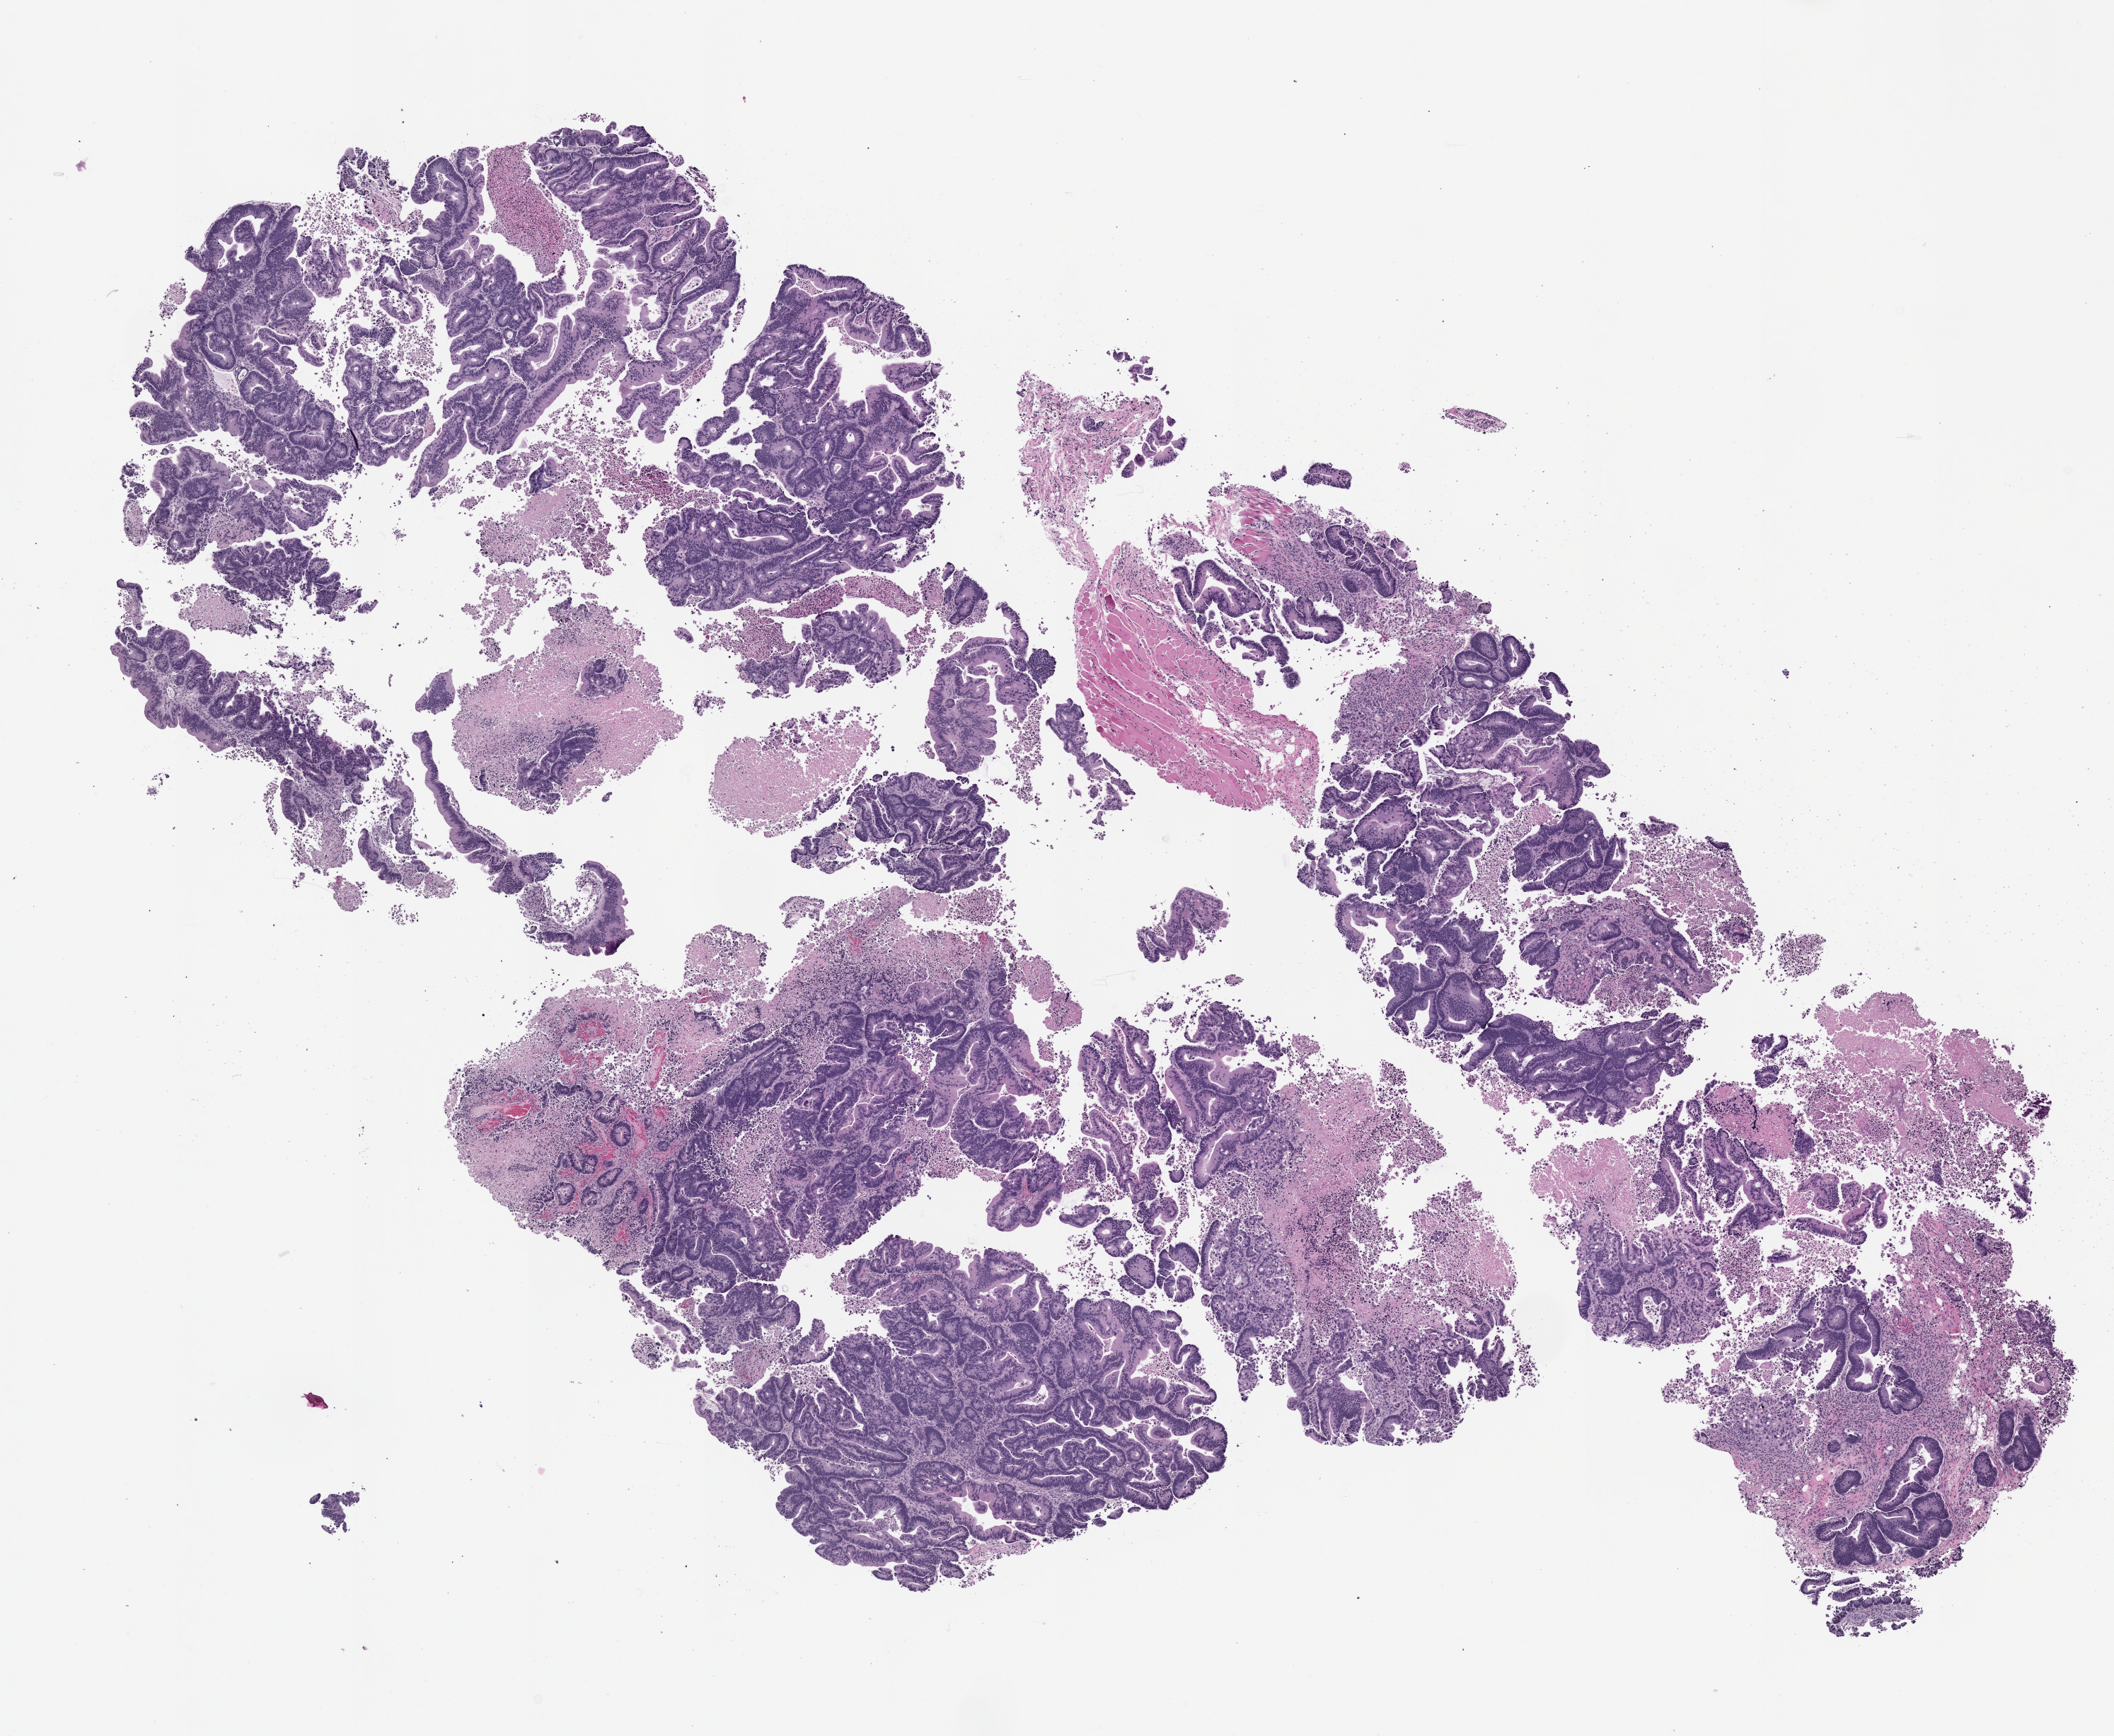
Haematoxylin and eosin whole-slide image of a patient-derived xenograft (PDX) tumor grown in a mouse, passage 1, low-resolution overview of the scanned area, about 12.0 x 9.9 mm, formalin-fixed paraffin-embedded section, originating tumor site category: gastrointestinal tract.
Originating patient diagnosis: Colorectal Carcinoma.